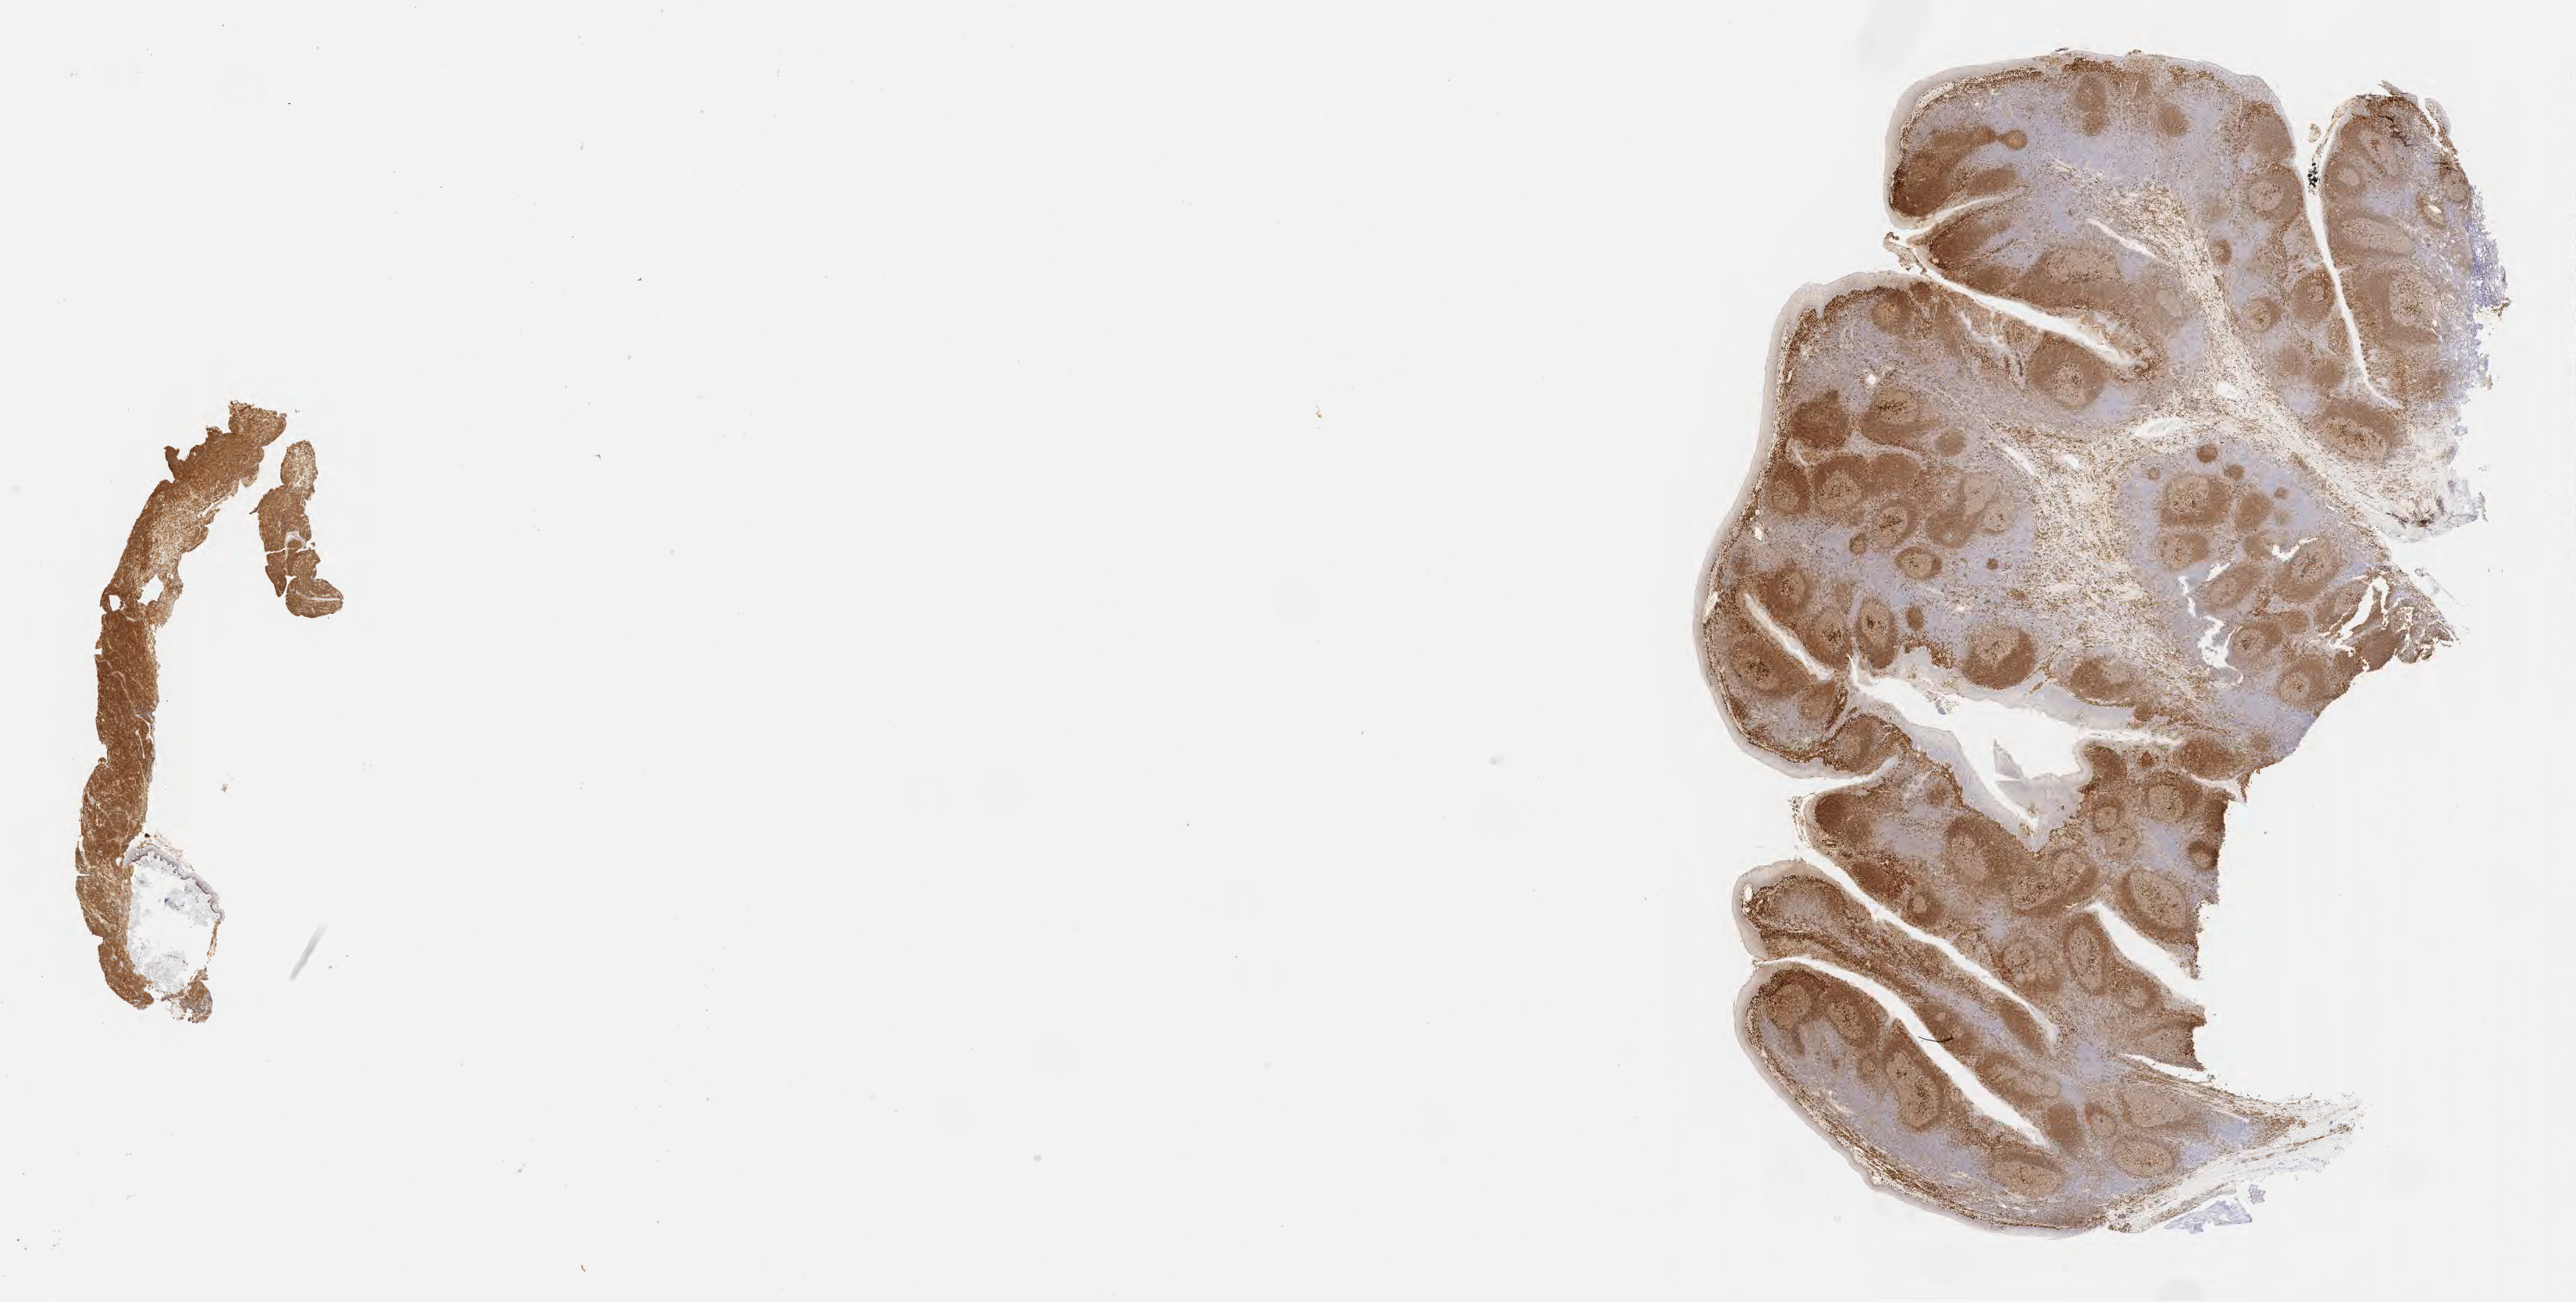
IHC for CD79a, whole-slide image — whole scanned area (about 26.7 x 13.5 mm) shown as a low-resolution overview, tumor tissue. Patient: female, 43 years old.
Histologic diagnosis: Diffuse large B-cell lymphoma, NOS.